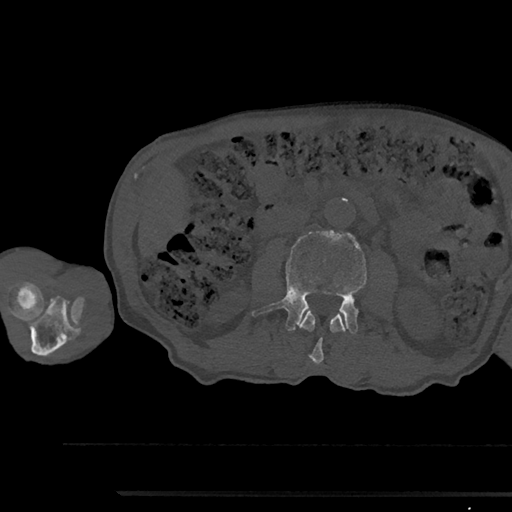
CT including the spine, one axial slice. Slice 518 of 797 in the series (ordered by position). 120 kVp. Bone window (W 1800 / L 400 HU). 0.5 mm slice thickness. 512 × 512 image matrix, field of view 367 × 367 mm. Male patient, age 79 years. From the clinical record (not read from this slice): primary cancer: prostate.
Structures marked on this image (semi-automatic segmentation, software-assisted and operator-edited):
- L2 vertebra: bounding box <299,310,347,364> (left, top, right, bottom; pixels)
- L3 vertebra: <252,231,366,334>